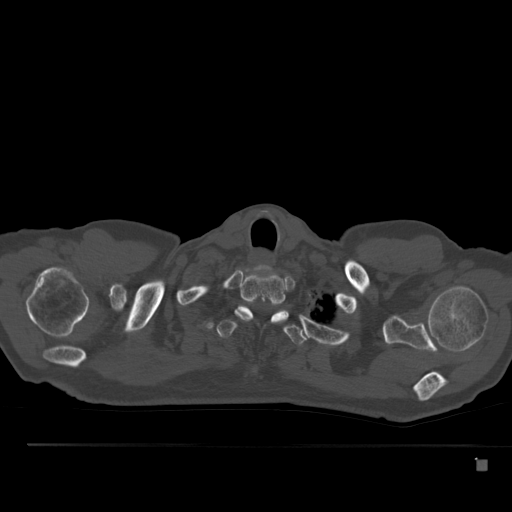
CT including the spine, one axial slice. Position 421 of 517 along the scan axis. Reconstruction kernel Br40s. Bone window (W 1800 / L 400 HU). 512 × 512 image matrix. Patient: male, 70 years. From the clinical record (not read from this slice): primary cancer: renal.
Structures marked on this image (semi-automatic segmentation, software-assisted and operator-edited):
- T1 vertebra: bounding box (x1, y1, x2, y2) in pixels: (235, 270, 288, 325)
- T2 vertebra: (217, 305, 308, 345)